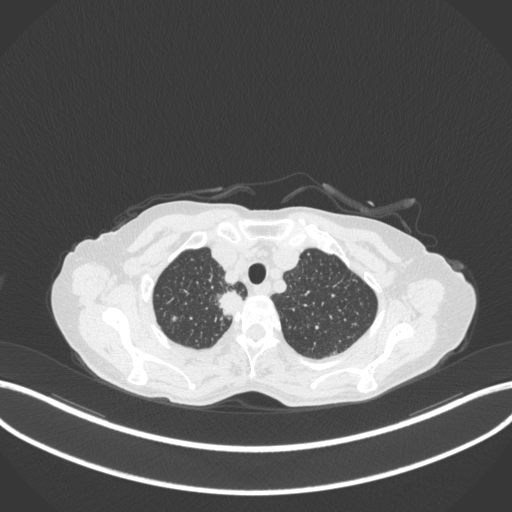
Chest CT, one axial slice. Position 320 of 363 along the scan axis. Lung window (W 1500 / L -600 HU). 1 mm slice thickness. 512 × 512 image matrix, field of view 400 × 400 mm. Patient: female, 75 years. Case-level facts recorded for this patient, not image findings: clinical TNM (as recorded): T1c N1 M1.
Structures marked on this image (bounding box drawn by a radiologist):
- lung tumour (recorded histology: adenocarcinoma): bounding box [x1, y1, x2, y2] px = [215, 286, 248, 321]